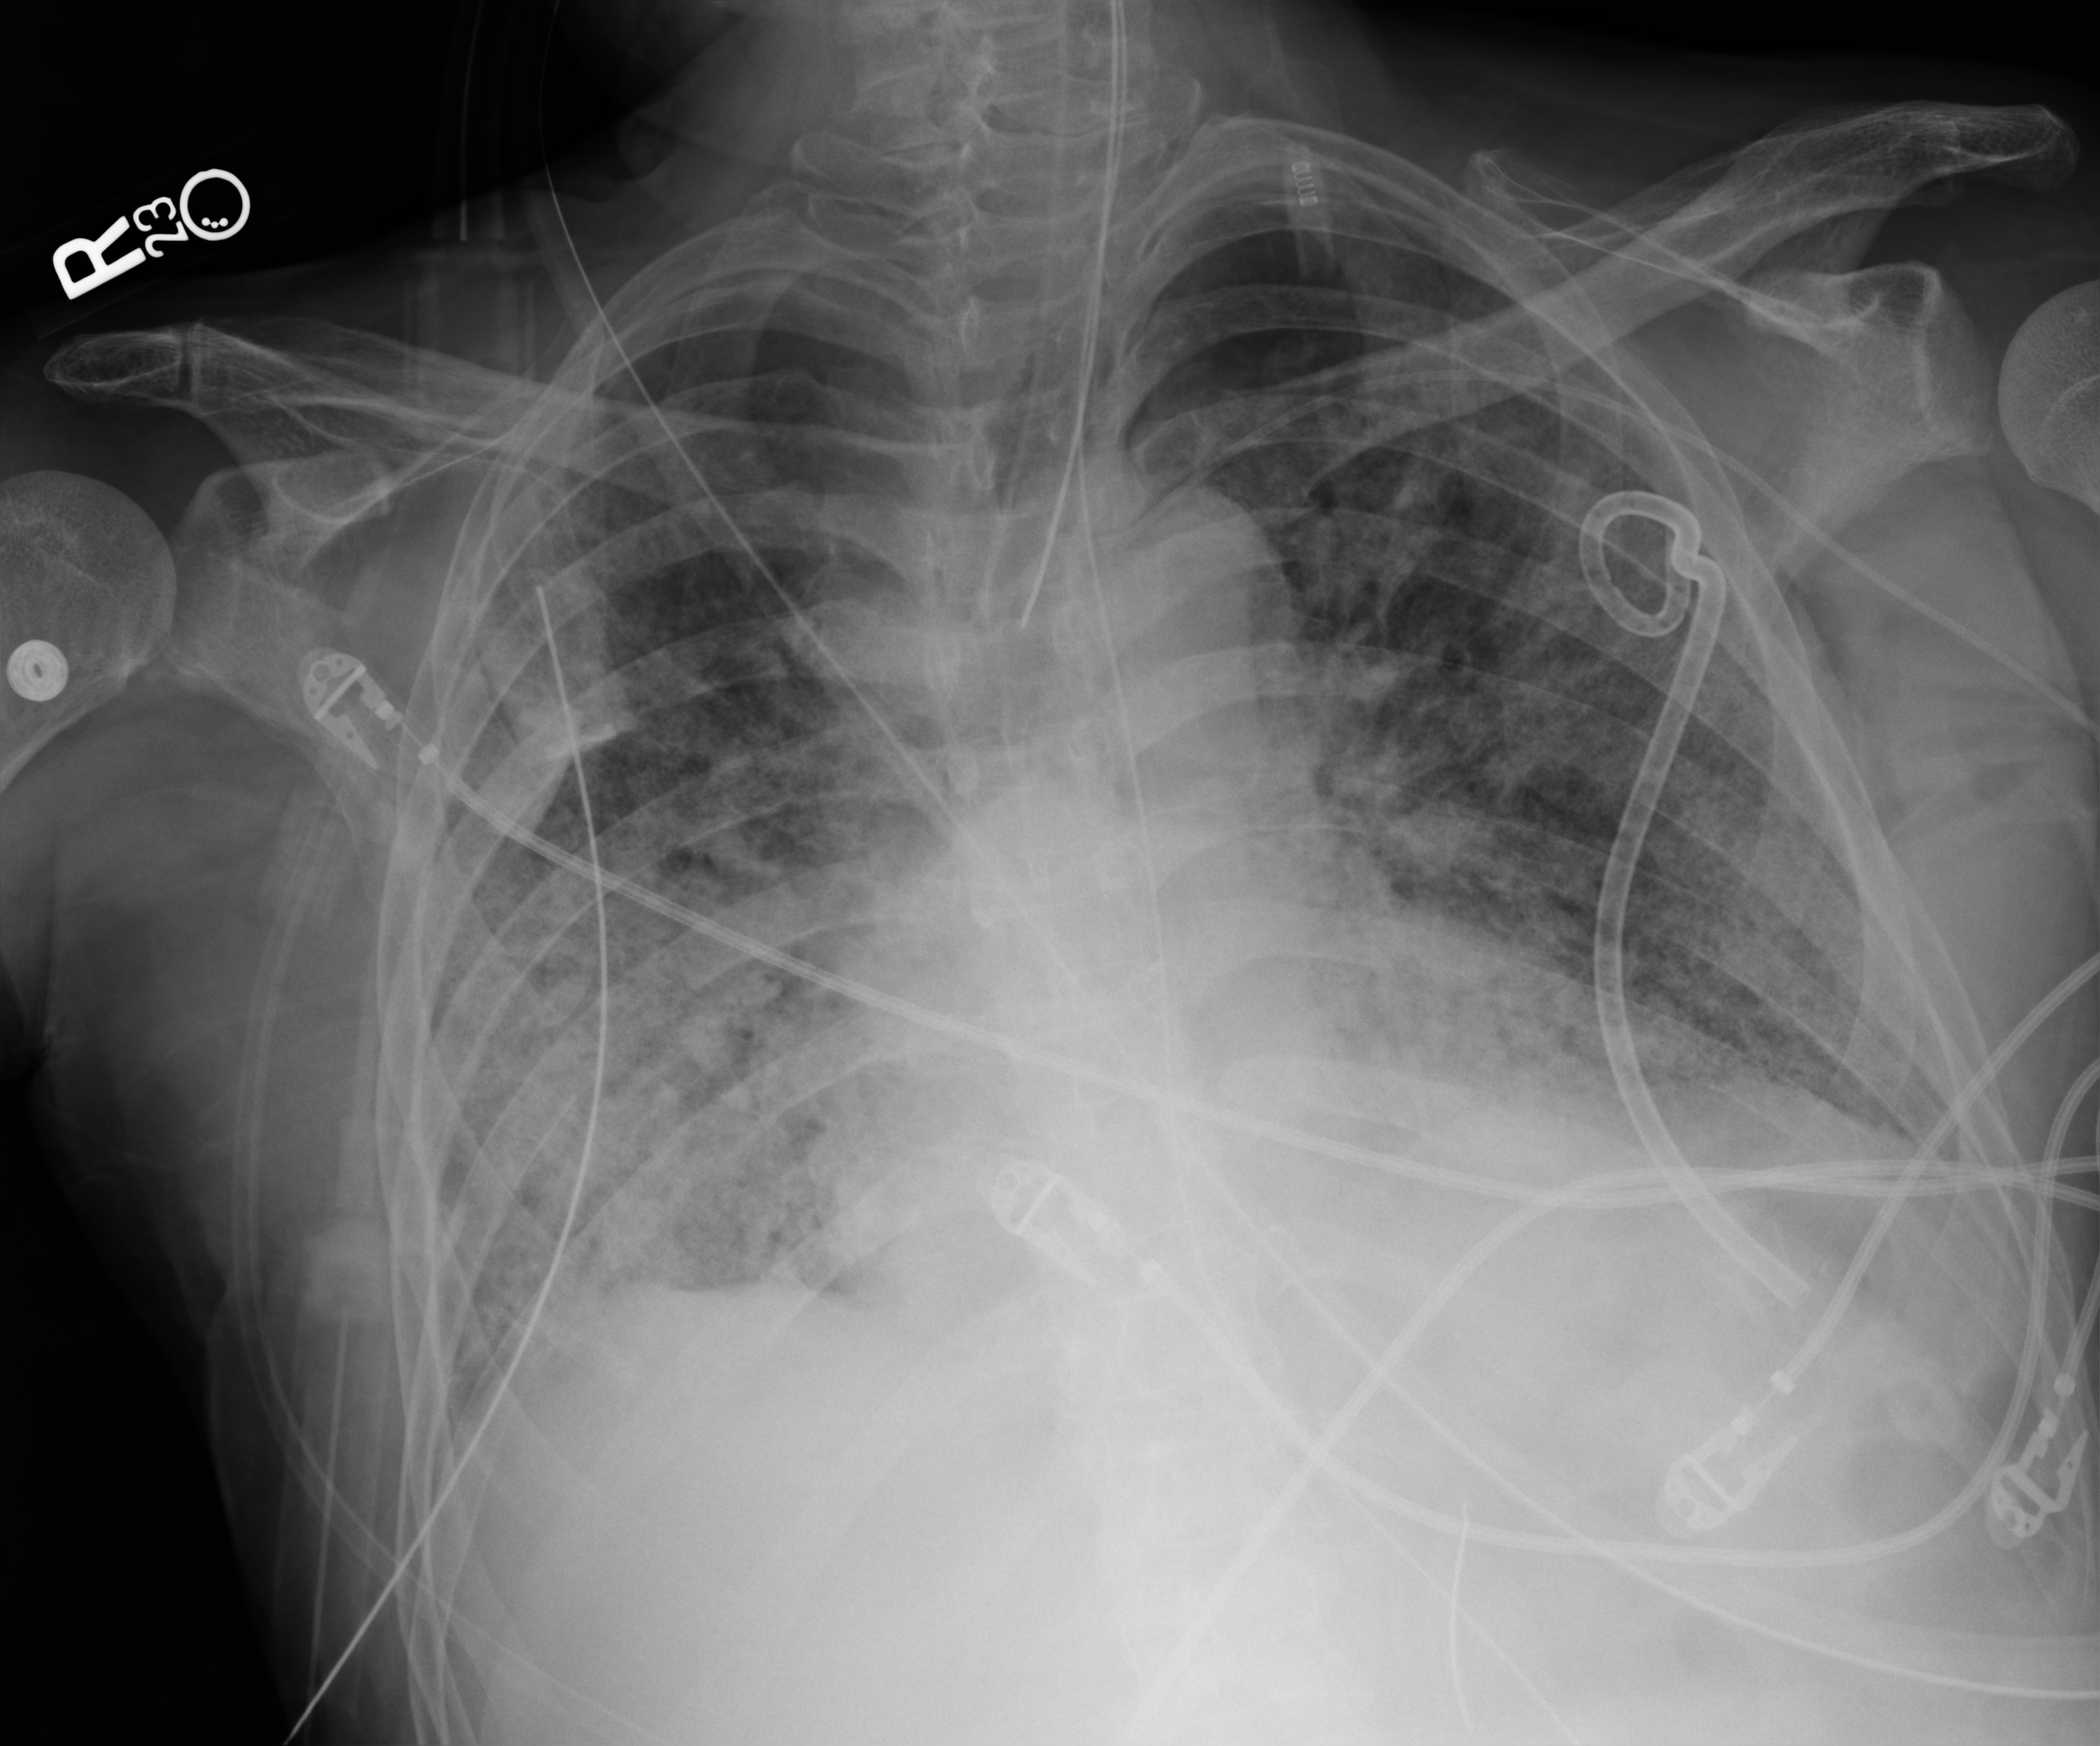
Portable chest radiograph, anteroposterior (AP) projection. Male patient hospitalised with COVID-19, age 60–74 years.
From the hospital-stay record, not from the radiograph (when in the stay this image was taken is not recorded):
- mechanically ventilated during this hospital stay: yes